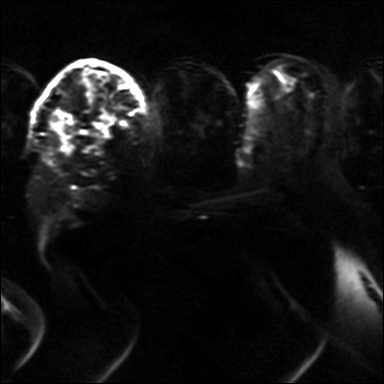
Breast MRI, one axial slice. Position 21 of 36 along the scan axis. Diffusion-weighted series; image 2 of 4 stored at this slice position (different b-values; order by instance number). 3 T. 4 mm slice thickness. 384 × 384 image matrix, field of view 320 × 320 mm. Female patient.
Structures marked on this image (manually delineated by an expert):
- tumour on diffusion-weighted imaging: box from (x=62, y=109) to (x=116, y=155) px